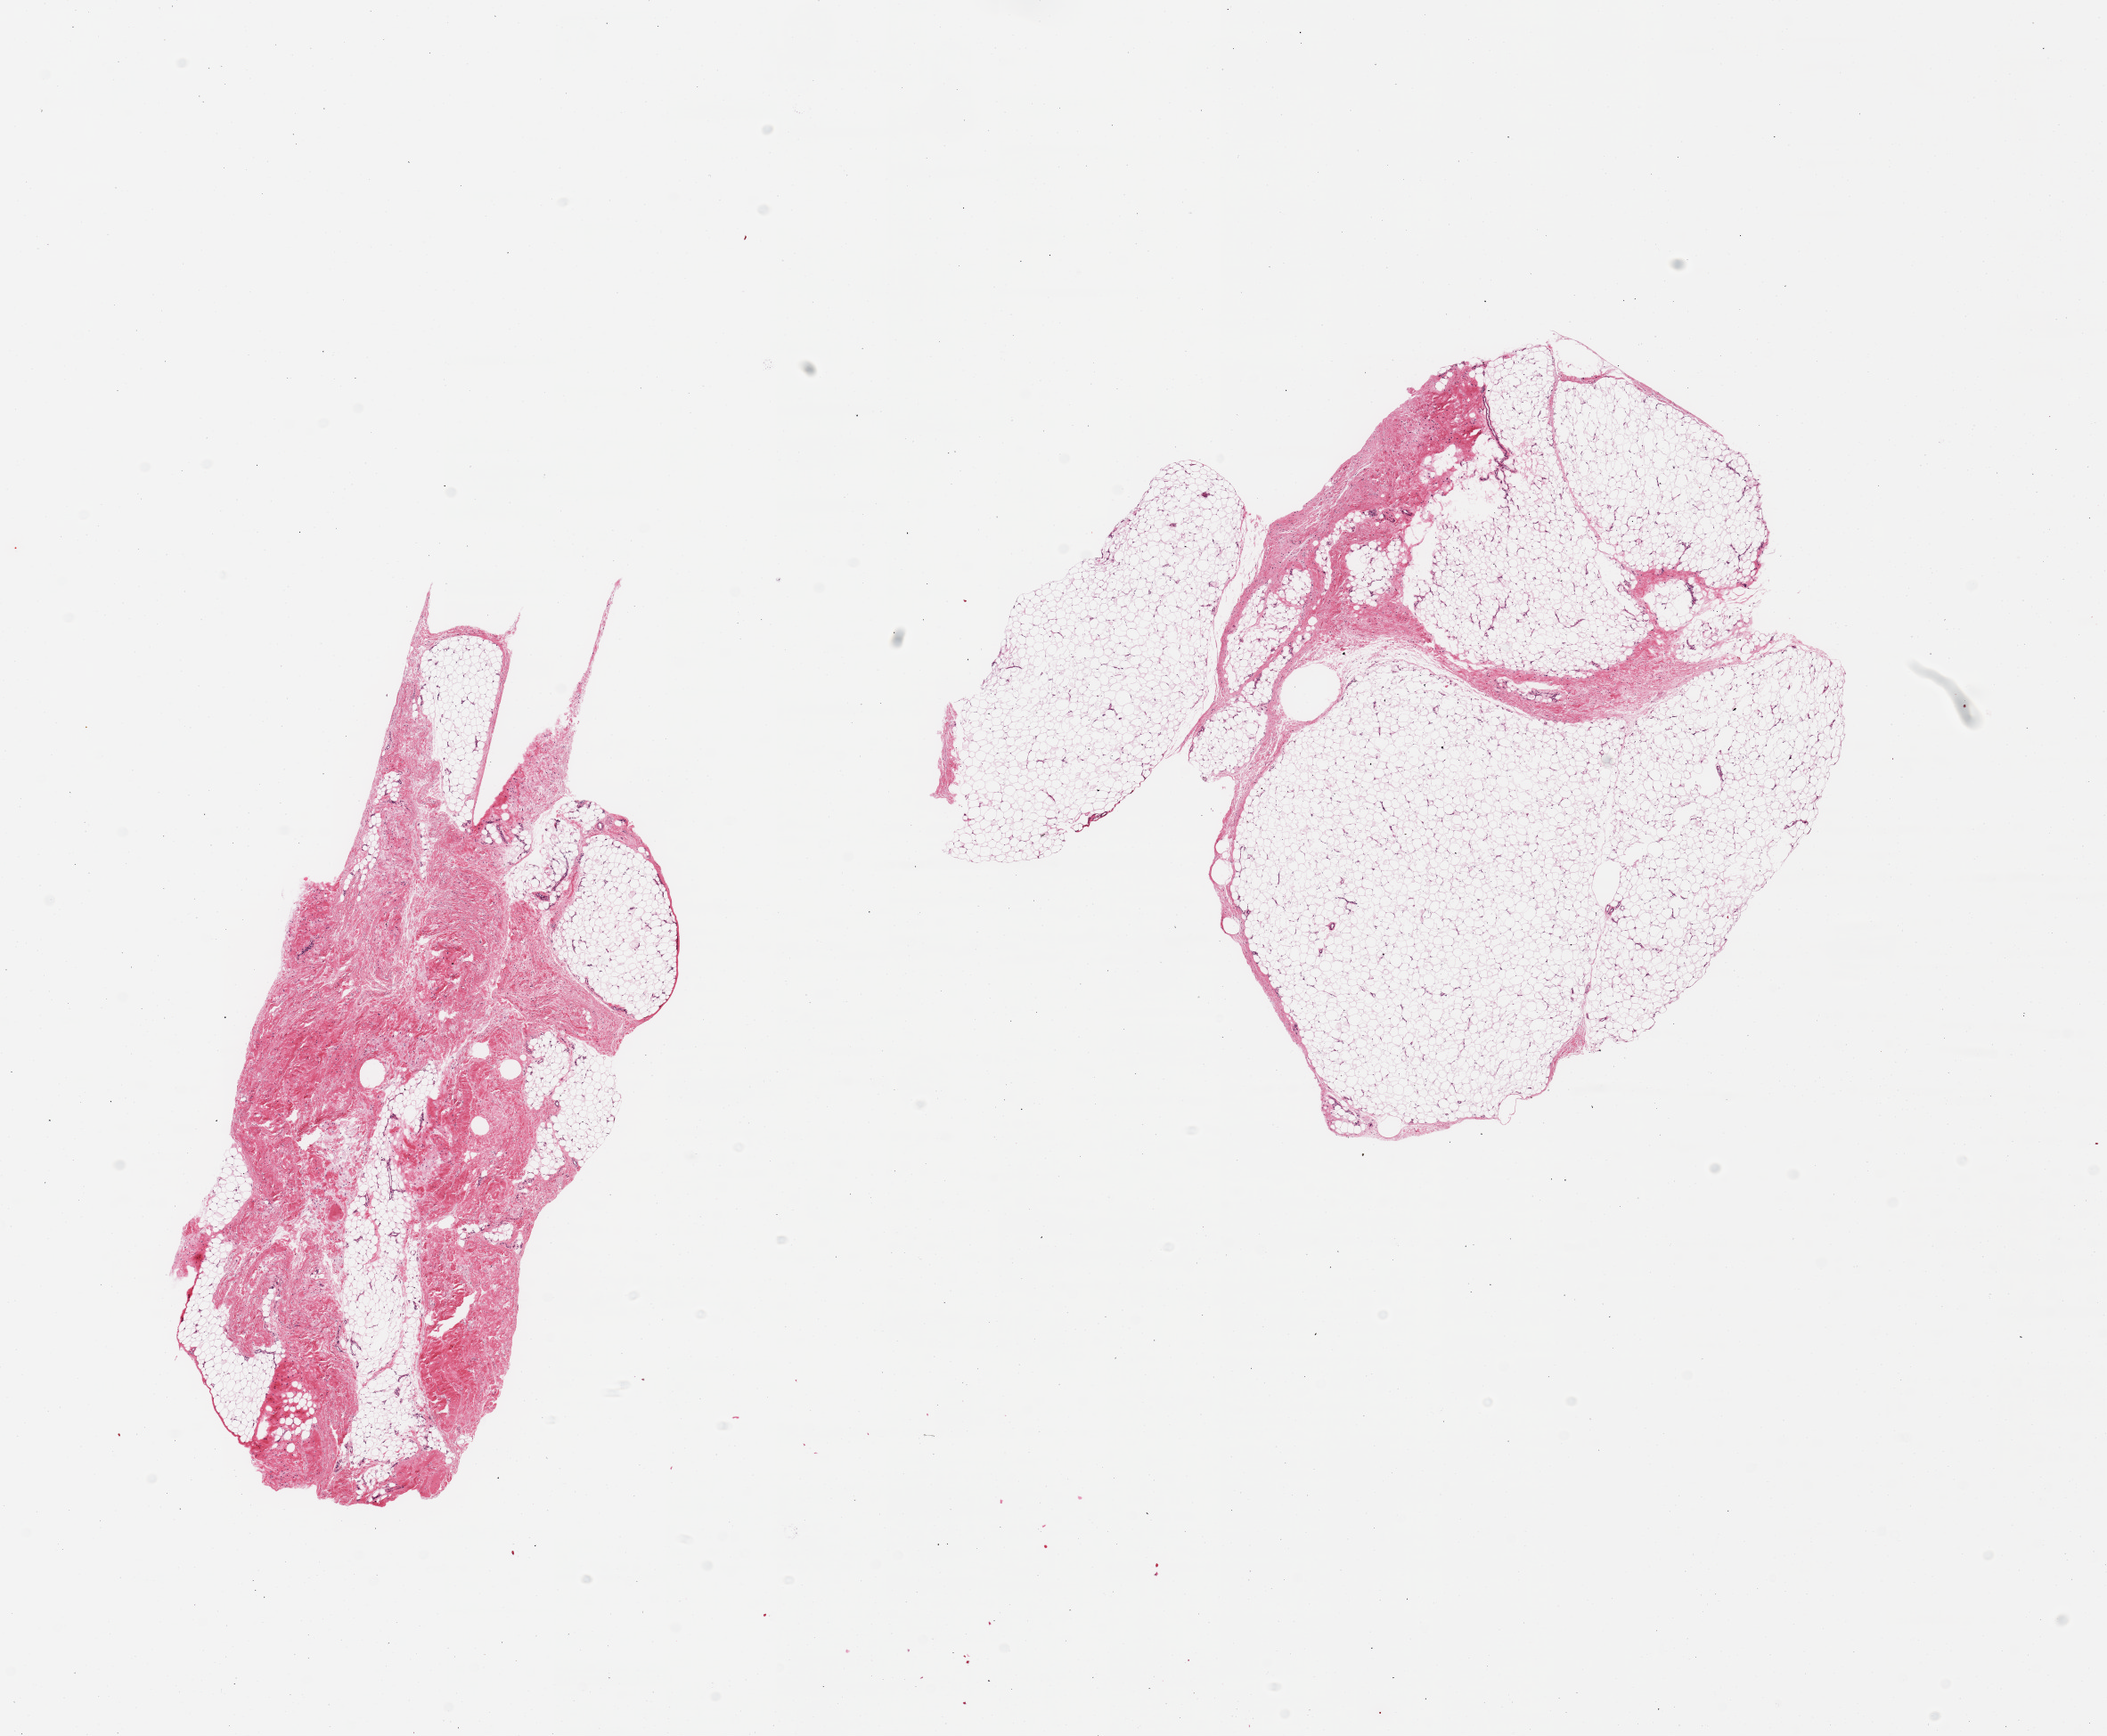
Haematoxylin and eosin whole-slide image, a low-resolution overview of the entire scanned area, about 18.7 x 15.4 mm (acquisition: 20x scan); PAXgene-fixed paraffin-embedded (PFPE) section; sampled site (target tissue): adipose tissue; donor tissue sample. Donor: female.
Review note (as recorded): 2 pieces; mature adipose tissue with 60% and 15% dense connective tissue component.